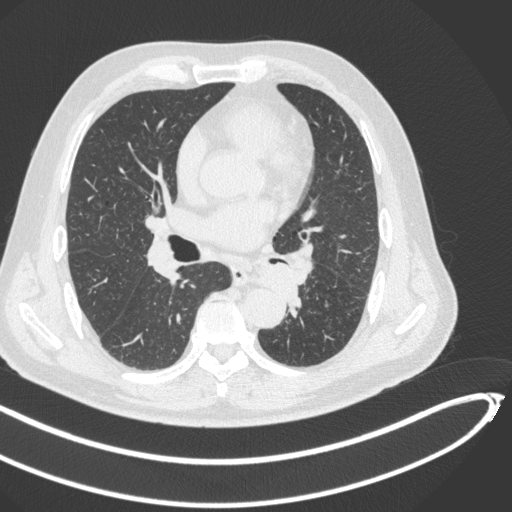
Chest CT, one axial slice. Slice 247 of 466 in the series (ordered by position). Reconstruction kernel B31f. Lung window (W 1500 / L -600 HU). 1 mm slice thickness. 512 × 512 image matrix, field of view 400 × 400 mm. Male patient, age 64 years. Case-level facts recorded for this patient, not image findings: clinical TNM (as recorded): T1c N0 M0; histopathological grade: G2.
Annotated regions visible in this slice (bounding box drawn by a radiologist):
- lung tumour (recorded histology: squamous cell carcinoma): bounding box <249,254,302,307> (left, top, right, bottom; pixels)